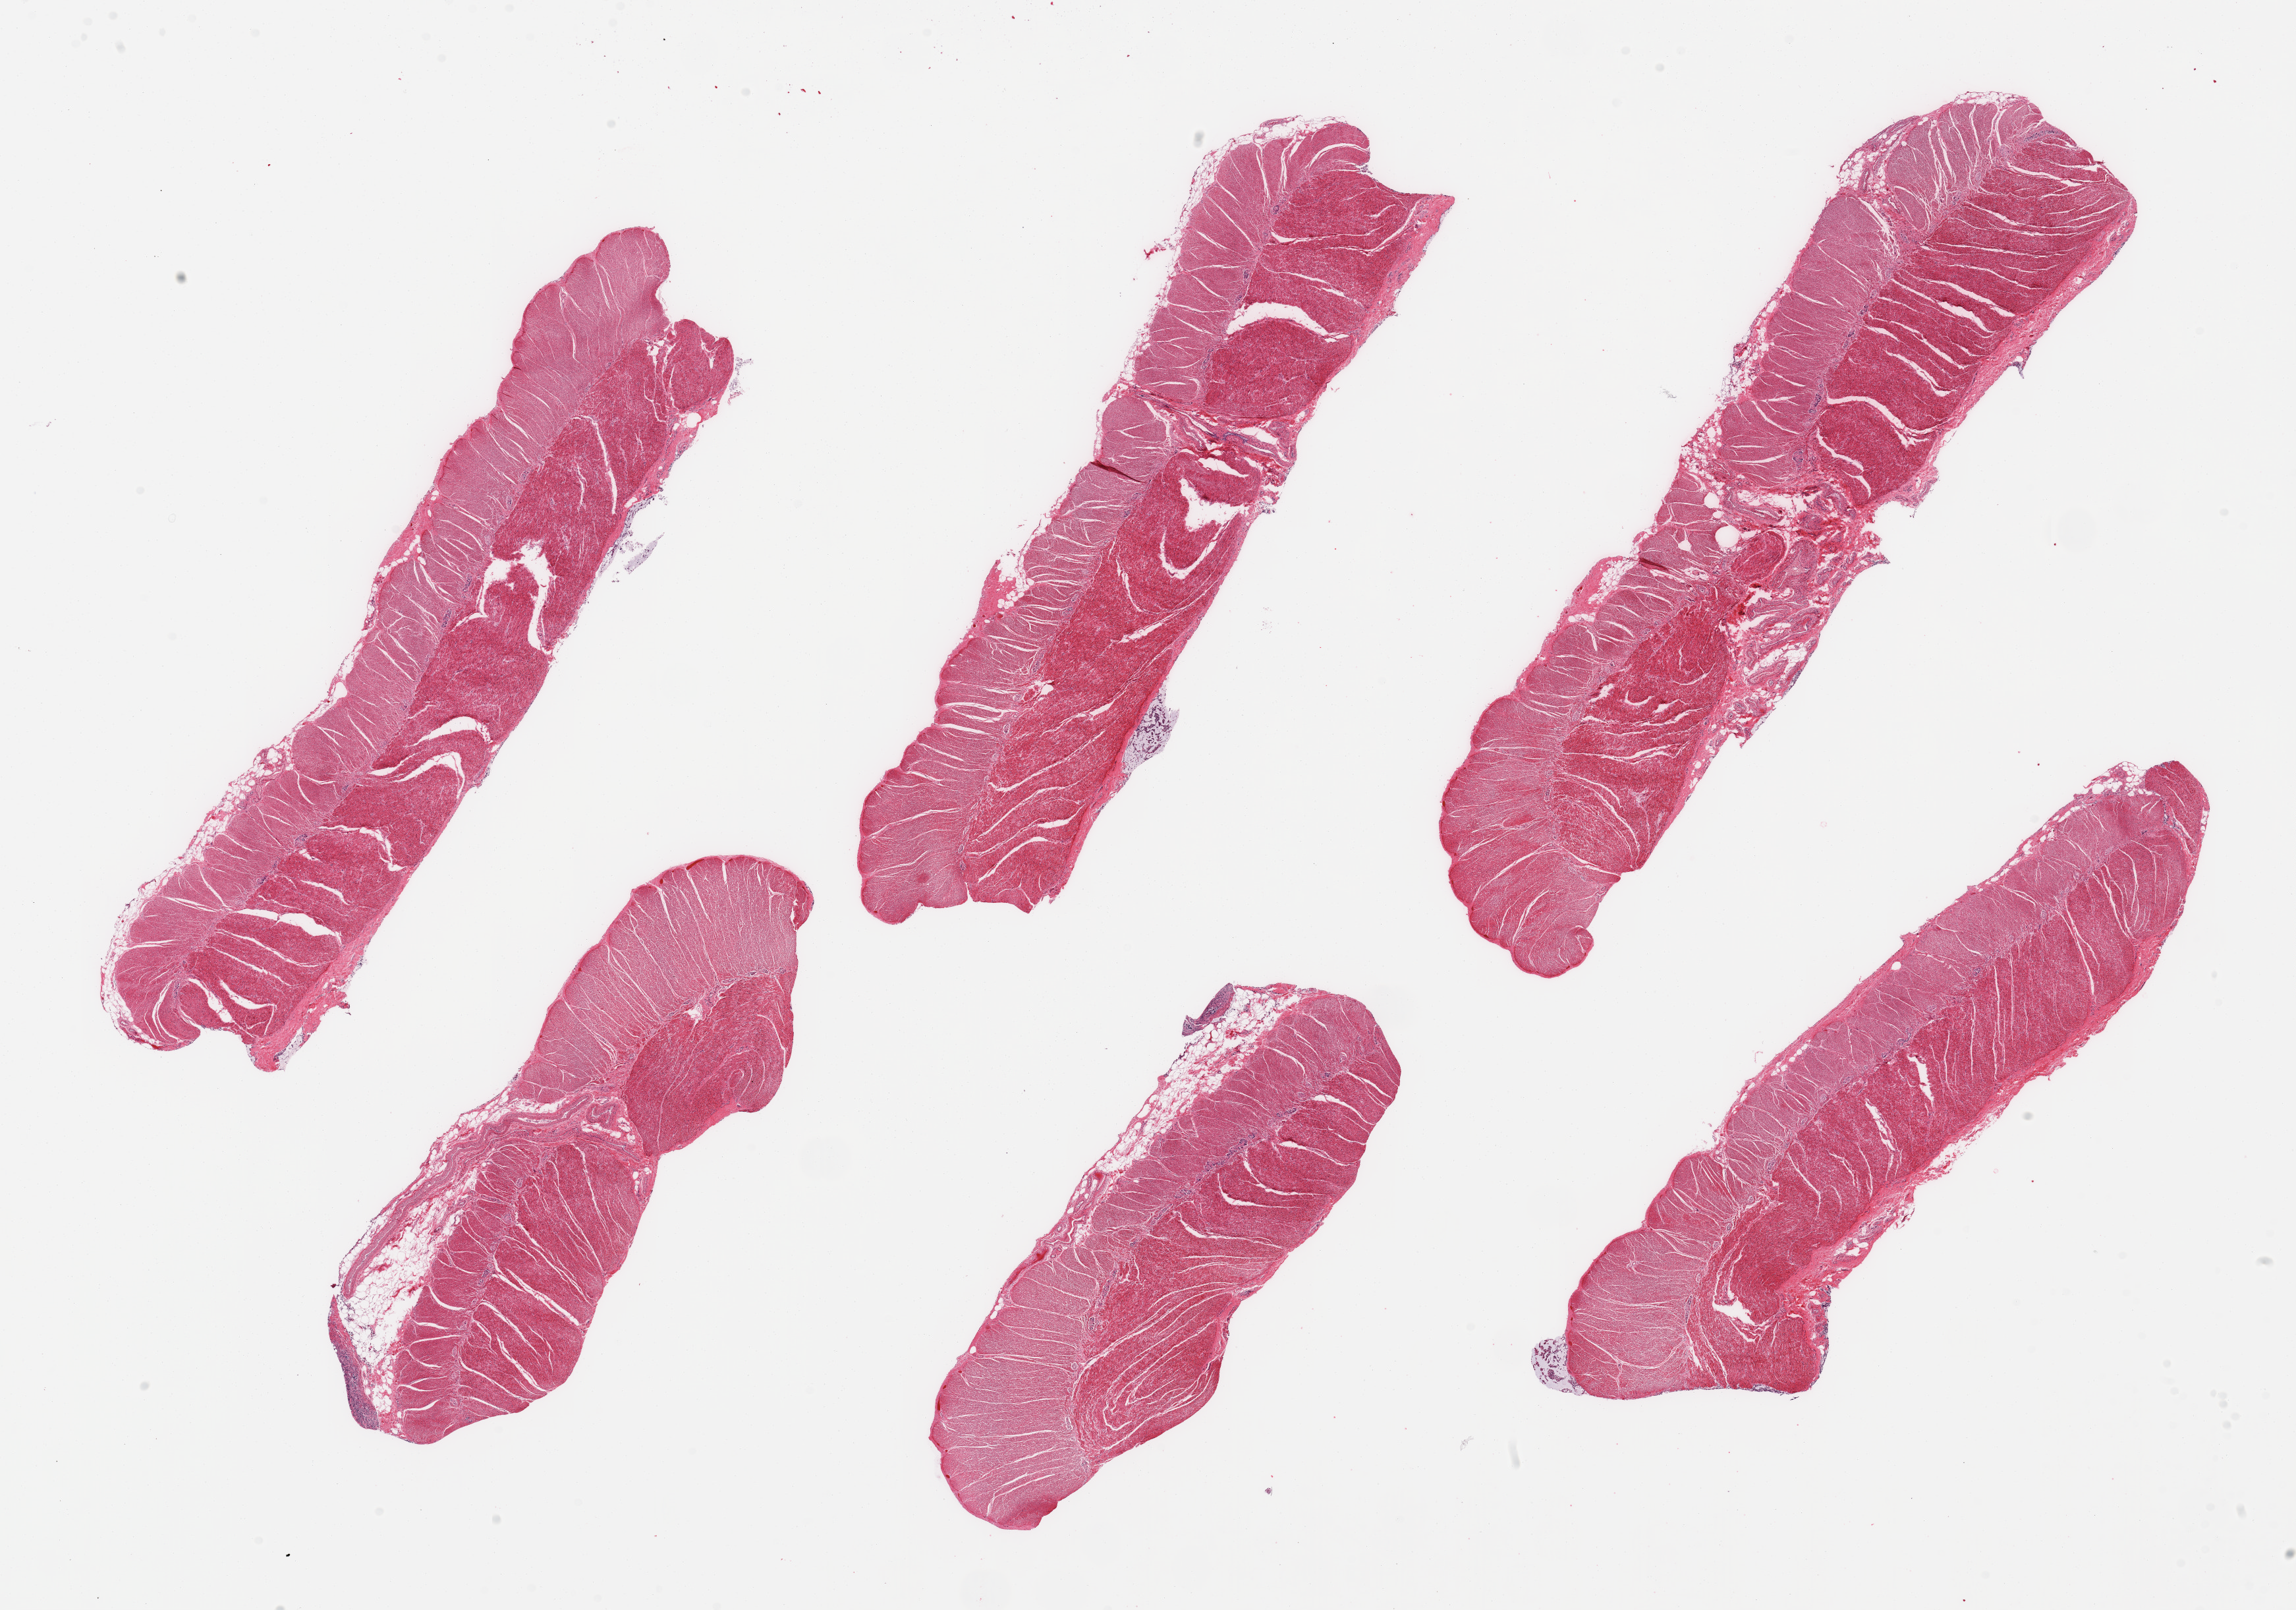
Whole-slide image, haematoxylin and eosin stain, brightfield, shown as a low-resolution overview of the whole scanned area (about 27.6 x 19.3 mm); PAXgene-fixed paraffin-embedded (PFPE) section; target tissue: sigmoid colon; tissue donor sample. Male donor.
Reviewer comment on this tissue sample: 6 pieces; target muscularis, some residual attached fat/vessels, portion of autolyzed mucosa.